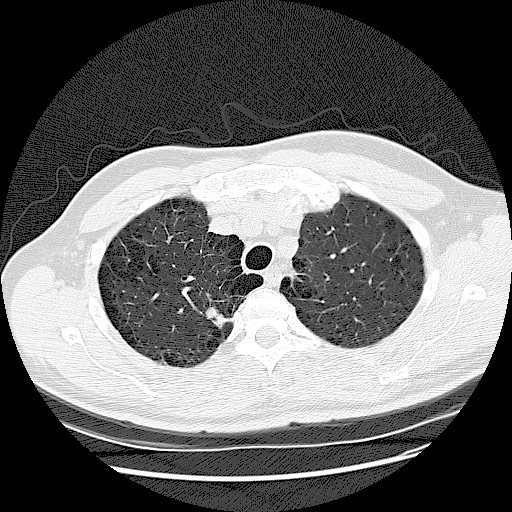
Low-dose screening chest CT, one axial slice. Slice 105 of 132 in the series (ordered by position). Reconstruction kernel LUNG. Lung window (W 1500 / L -600 HU). 512 × 512 image matrix, field of view 380 × 380 mm.
Annotated regions visible in this slice (outlined manually by an expert reader):
- lesion 1 (tumor, upper lobe of right lung): bounding box (x1, y1, x2, y2) in pixels: (205, 307, 234, 329)